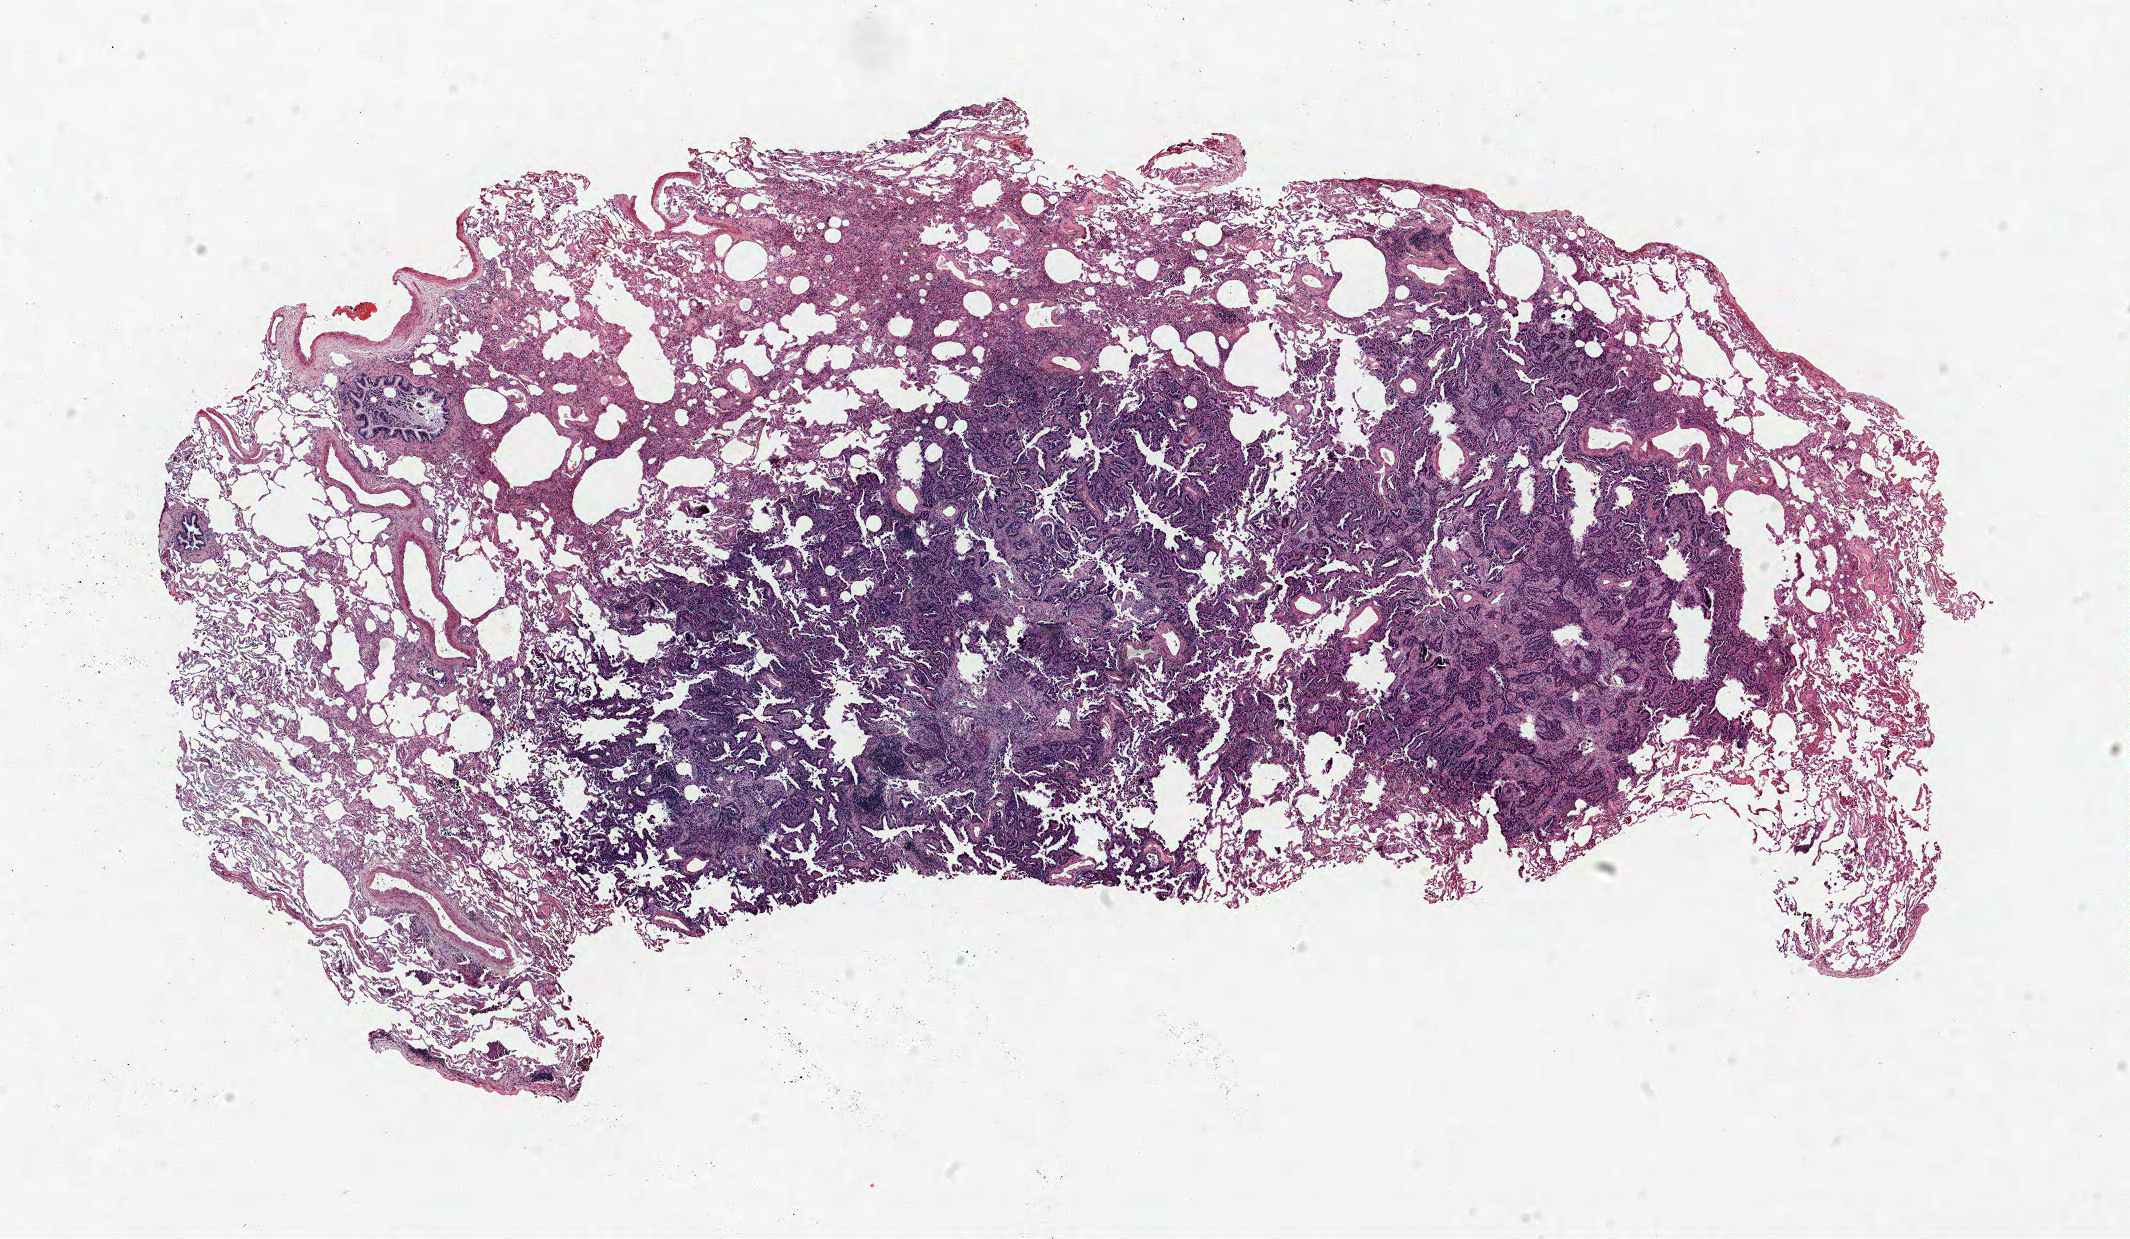
Whole-slide histology image, H&E, whole scanned area (about 17.0 x 9.9 mm, acquisition: 40x scan) shown as a low-resolution overview; formalin-fixed paraffin-embedded (FFPE) section; lung. Male, age 65 at enrolment. Current smoker at enrolment. Grade: poorly differentiated (G3).
Participant's lung-cancer diagnosis: Adenocarcinoma, NOS. Primary tumour location (clinical record): right lower lobe. Tumour size (pathology): 10 mm. Stage (AJCC 6th edition): IA.